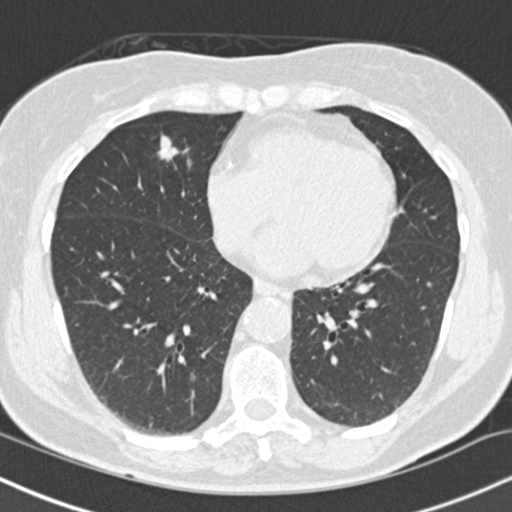
Axial slice from a low-dose chest CT screening exam, baseline annual screen, lung window (W 1500 / L -600 HU), standard (soft-tissue) reconstruction kernel (B30f), slice 88 of 145 in the series, 512 × 512 image matrix, field of view 320 × 320 mm. Female participant, aged 66 years at enrolment. Current smoker at enrolment.
Expert reader's lesion annotation, box from (x=141, y=128) to (x=186, y=170) px. The exam's reader record, not a measurement of the box and not confirmed to be the same lesion: non-calcified nodule or mass ≥4 mm, right lower lobe, 10 × 8 mm, smooth margins, soft tissue attenuation. Lung cancer was diagnosed 96 days after this screen: squamous cell carcinoma, keratinizing, NOS, right upper lobe, right middle lobe, poorly differentiated (G3), stage IA (AJCC 6th edition), 14 mm at pathology.